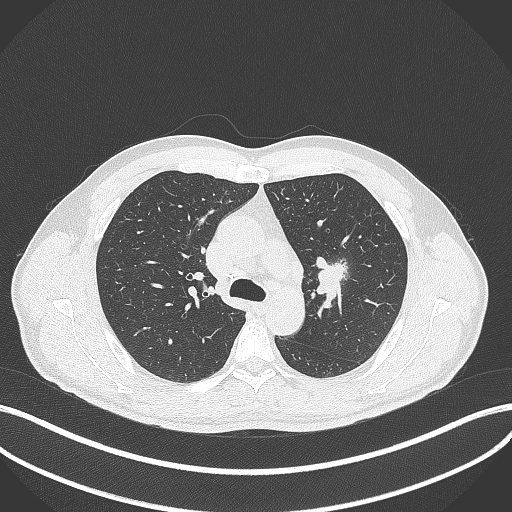
Chest CT, one axial slice; position 286 of 392 along the scan axis; 120 kVp; lung window (W 1500 / L -600 HU); 1 mm slice thickness; 512 × 512 image matrix. Male patient, age 50 years. From the clinical record (not read from this slice): clinical TNM (as recorded): T1c N1 M1b.
Structures marked on this image (rectangle marked by the reading radiologist):
- lung tumour (recorded histology: squamous cell carcinoma): bounding box [x1, y1, x2, y2] px = [316, 253, 348, 298]